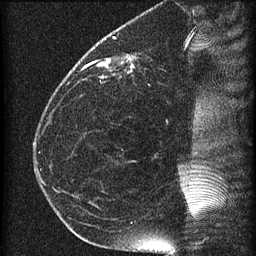
Breast MRI (dynamic contrast-enhanced), one sagittal slice; position 22 of 60 along the scan axis; dynamic contrast-enhanced series, image 2 of 4 at this slice position (ordered by acquisition); 1.5 T; TE 4.2 ms, TR 22.7 ms; 256 × 256 image matrix, field of view 180 × 180 mm. Female patient, age 35 years. Case-level facts recorded for this patient, not image findings: setting: breast cancer imaged before/during neoadjuvant chemotherapy; receptor status: HR-positive, HER2-negative.
Annotated regions visible in this slice (semi-automatically segmented with operator editing):
- analysis volume of interest (the breast-tissue region the enhancement analysis was run in; not a lesion): bounding box (x1, y1, x2, y2) in pixels: (69, 27, 199, 112)
- tumour enhancement mask (voxels above the 90 % enhancement threshold inside the analysis volume of interest): (83, 55, 135, 72)